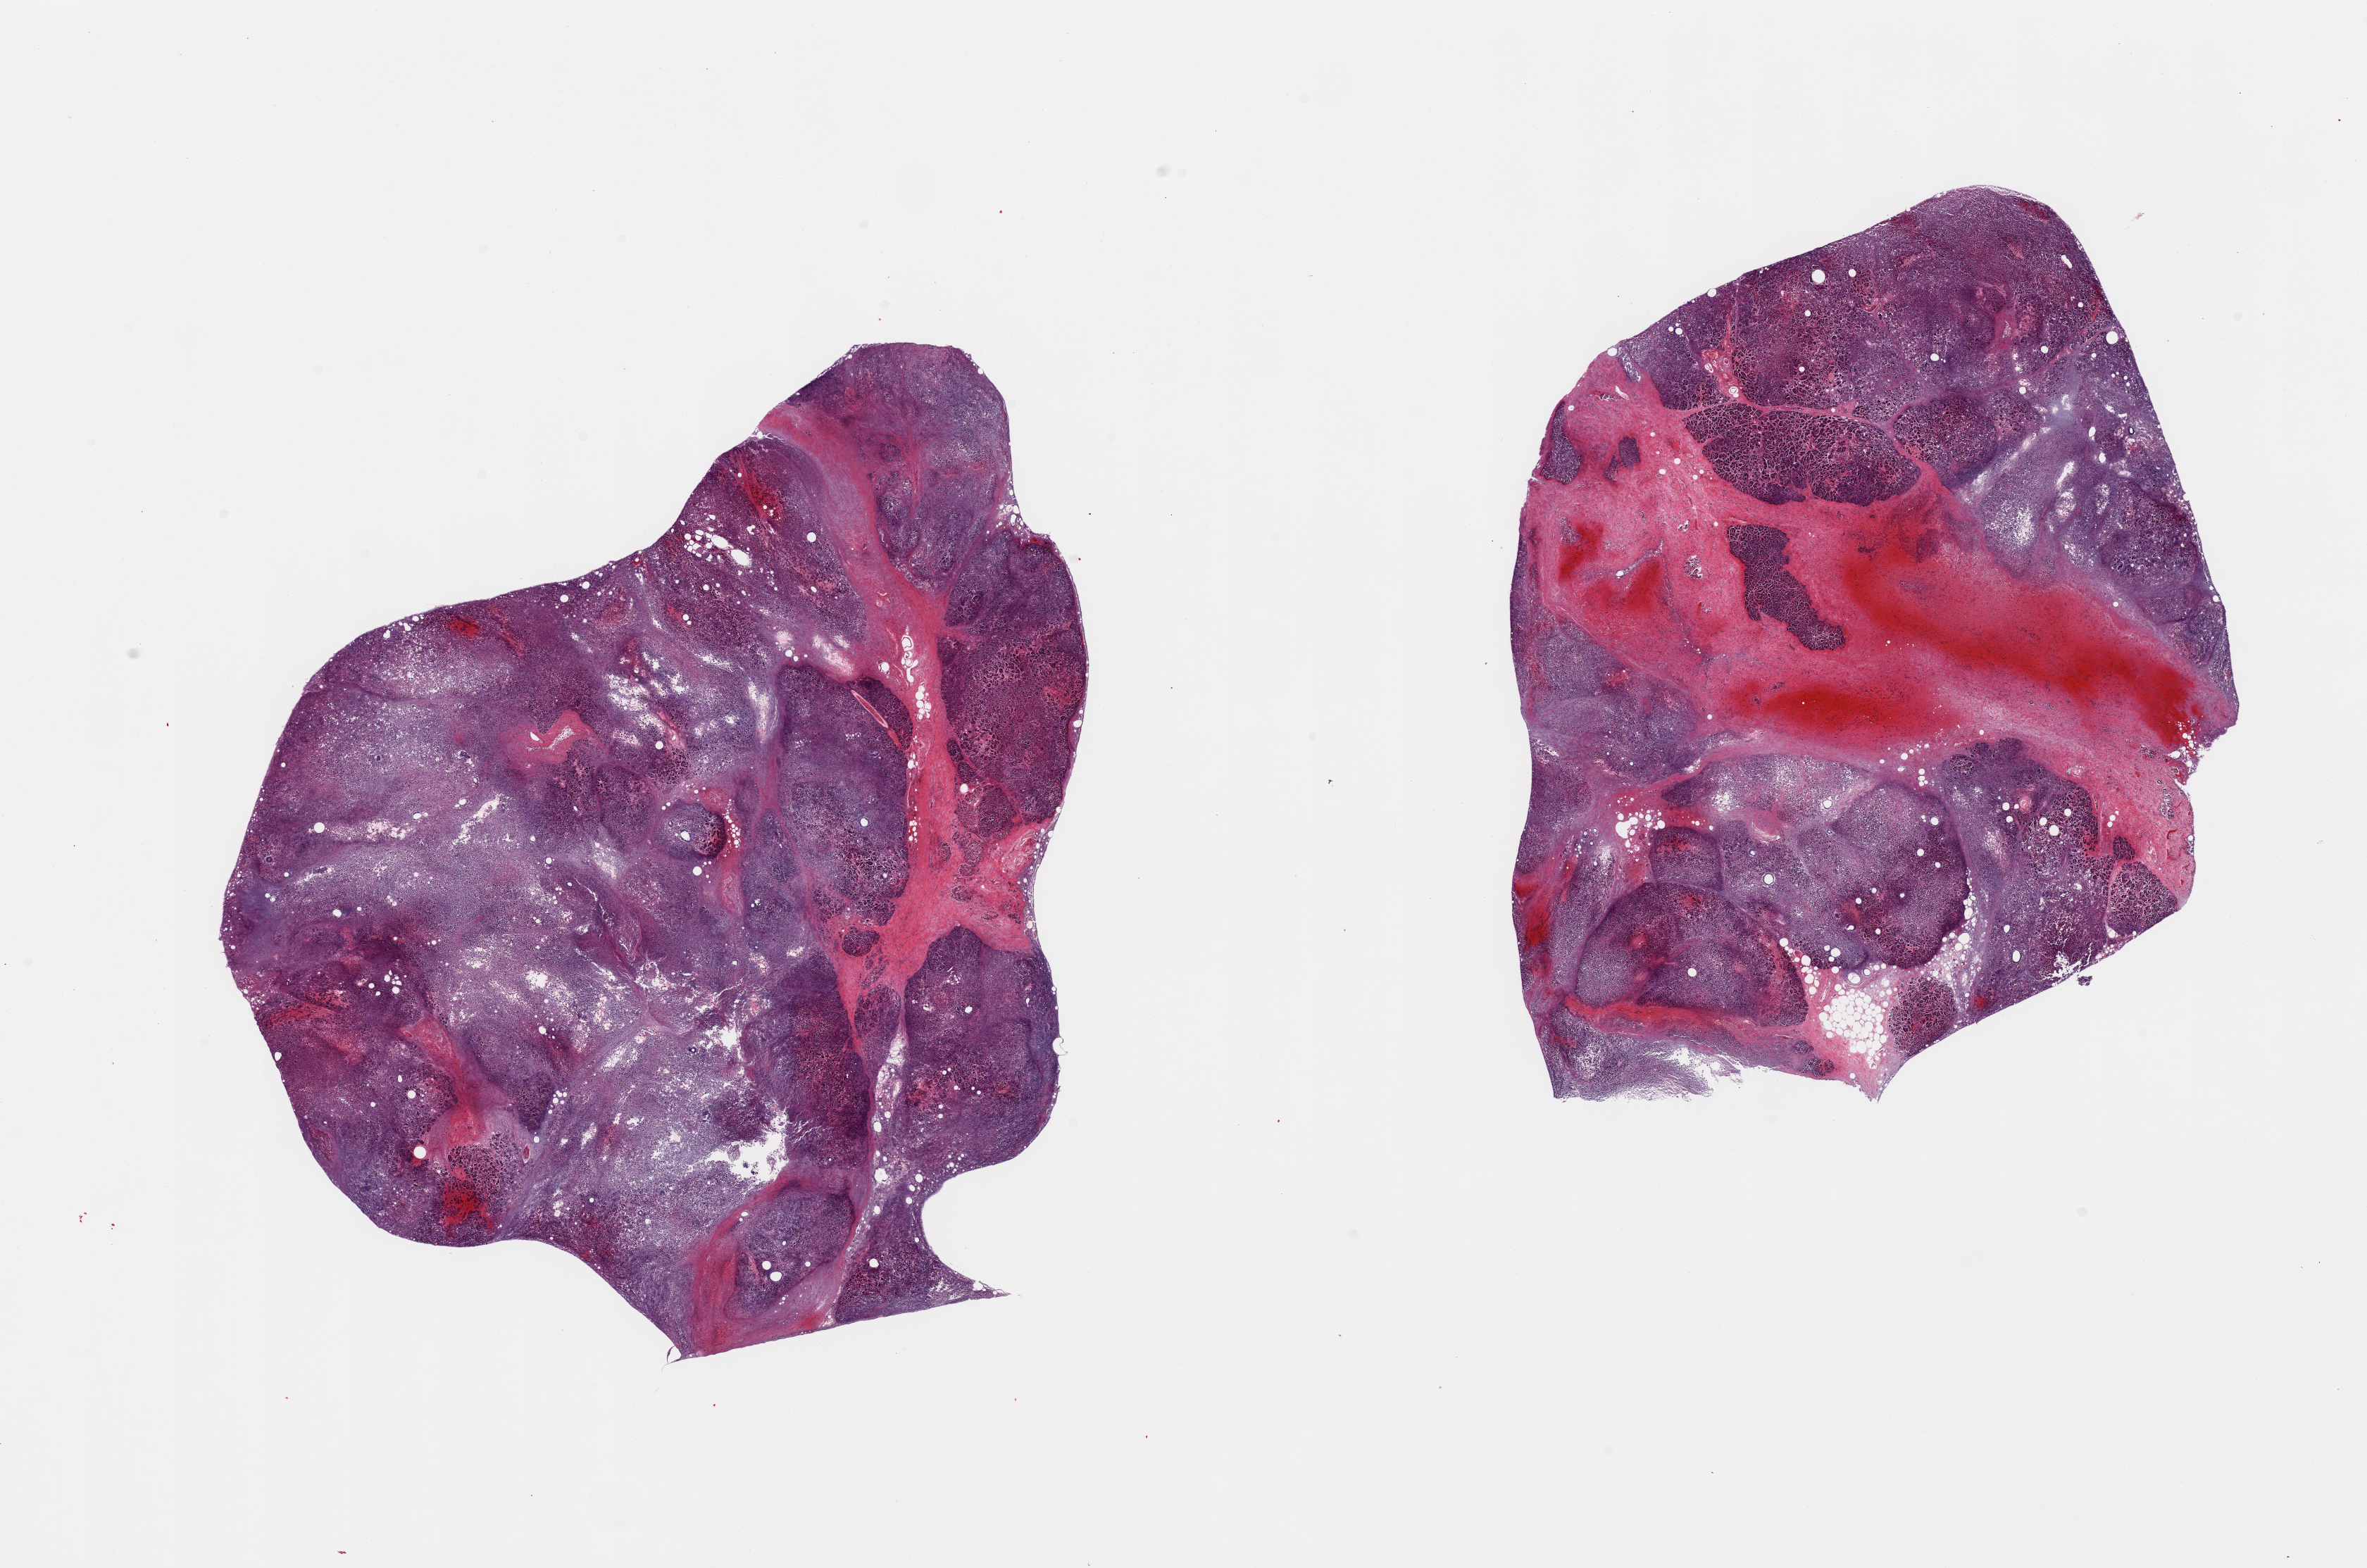
Hematoxylin and eosin (H&E) whole-slide image — shown as a low-resolution overview of the whole scanned area (about 26.6 x 17.6 mm, acquisition: 20x scan). PAXgene-fixed, paraffin-embedded tissue. Sampled site (target tissue): pancreas. Tissue donor sample.
Review note (as recorded): 2 pieces; severe autolysis.